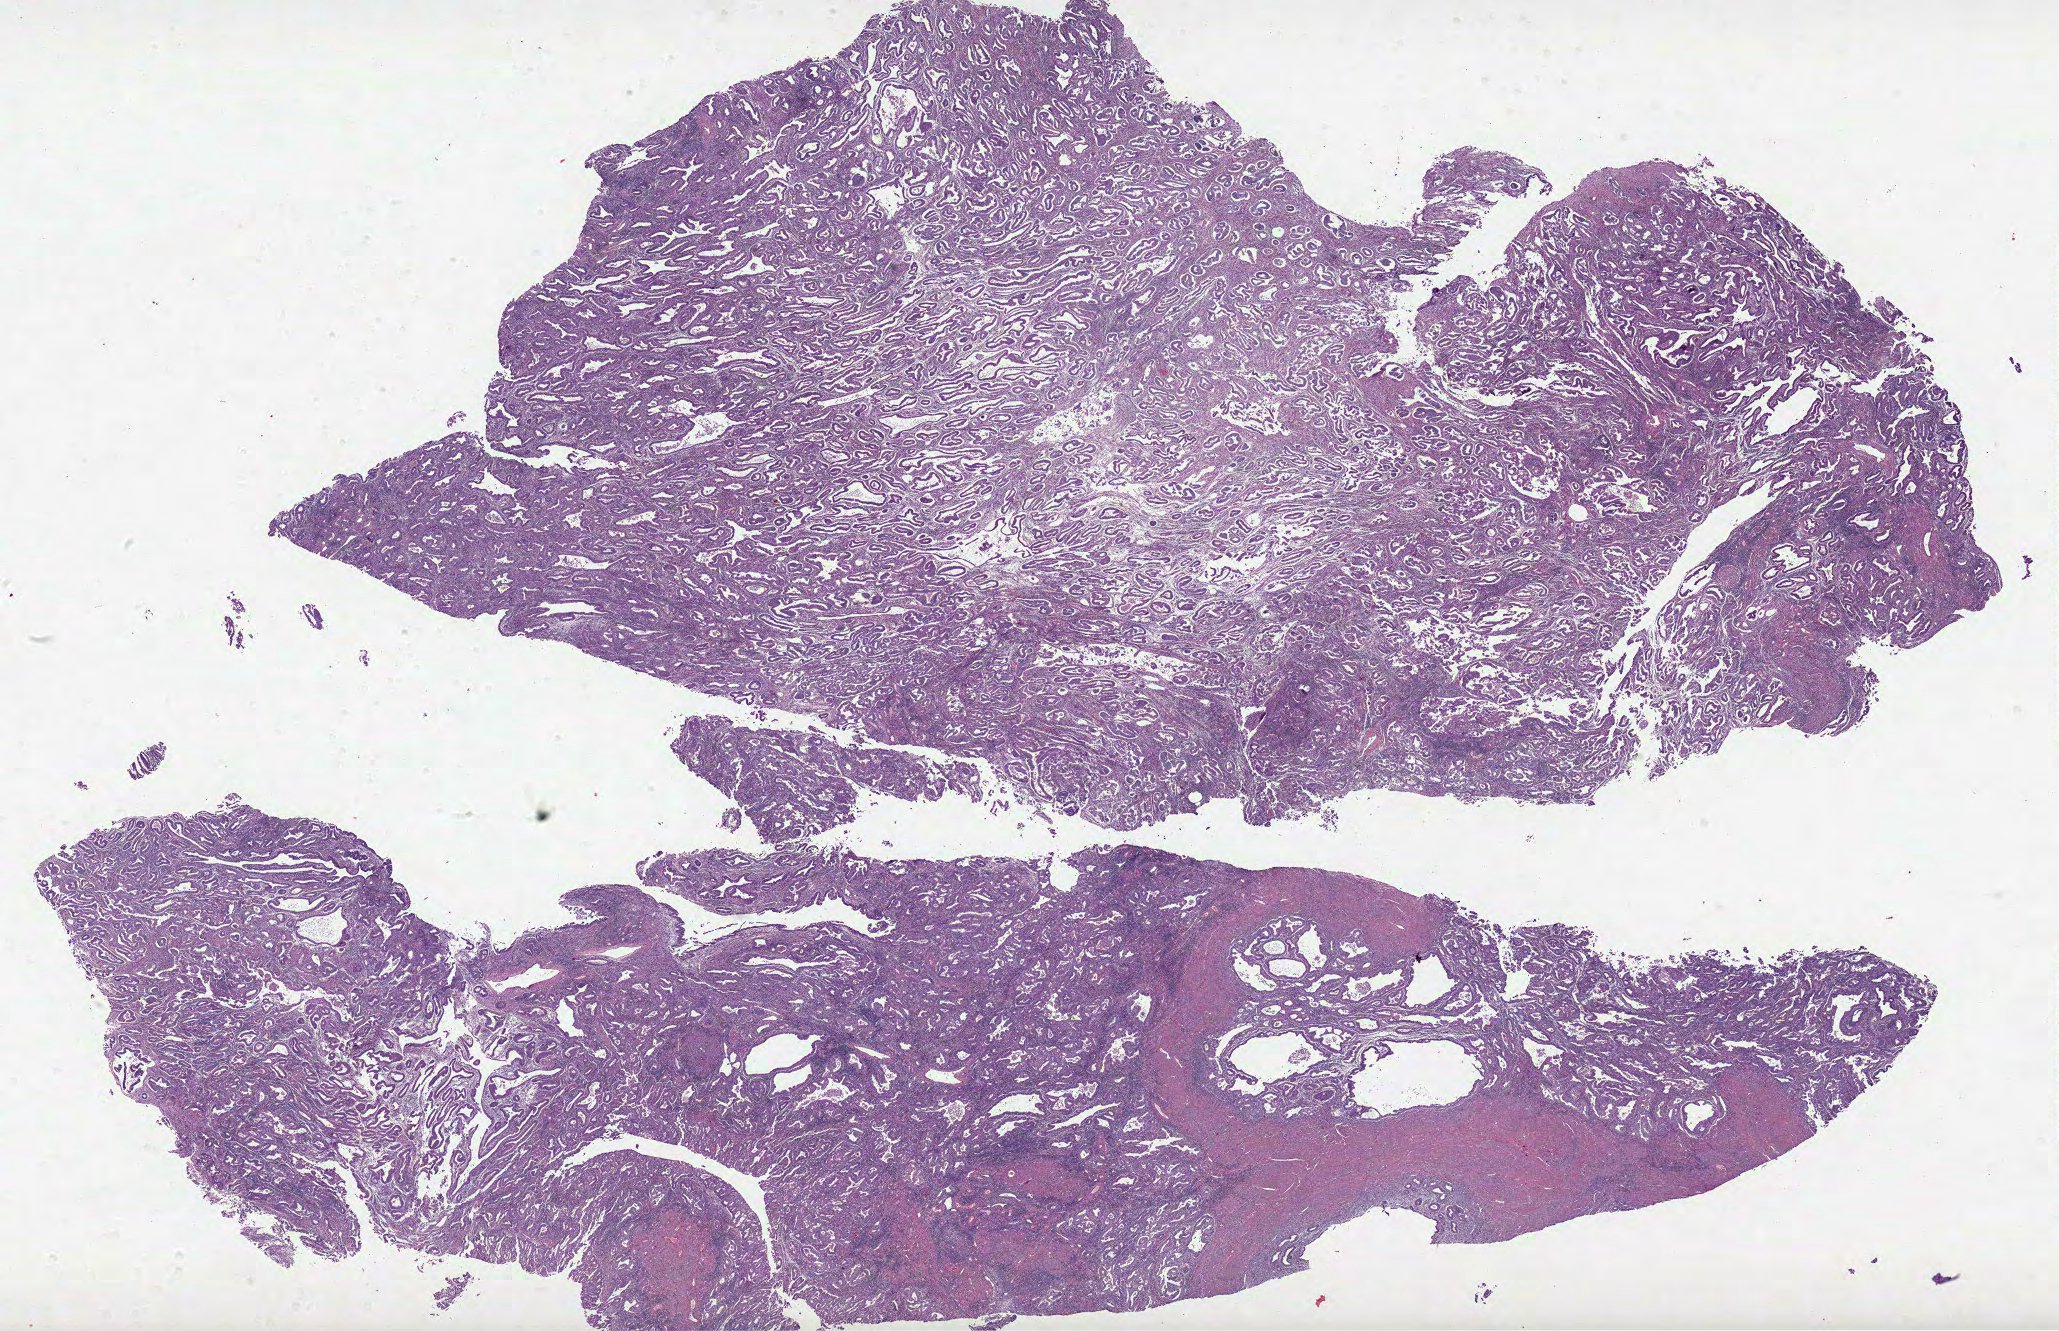
Whole-slide histology image, H&E, whole scanned area (about 32.8 x 21.2 mm, acquisition: 20x scan) shown as a low-resolution overview, formalin-fixed paraffin-embedded (FFPE) diagnostic section, uterus, primary tumour sample. Female, age 42 years at initial diagnosis. Histologic grade: G1 (well differentiated).
FIGO stage: IA. Histologic diagnosis: Endometrioid adenocarcinoma, NOS (endometrium).